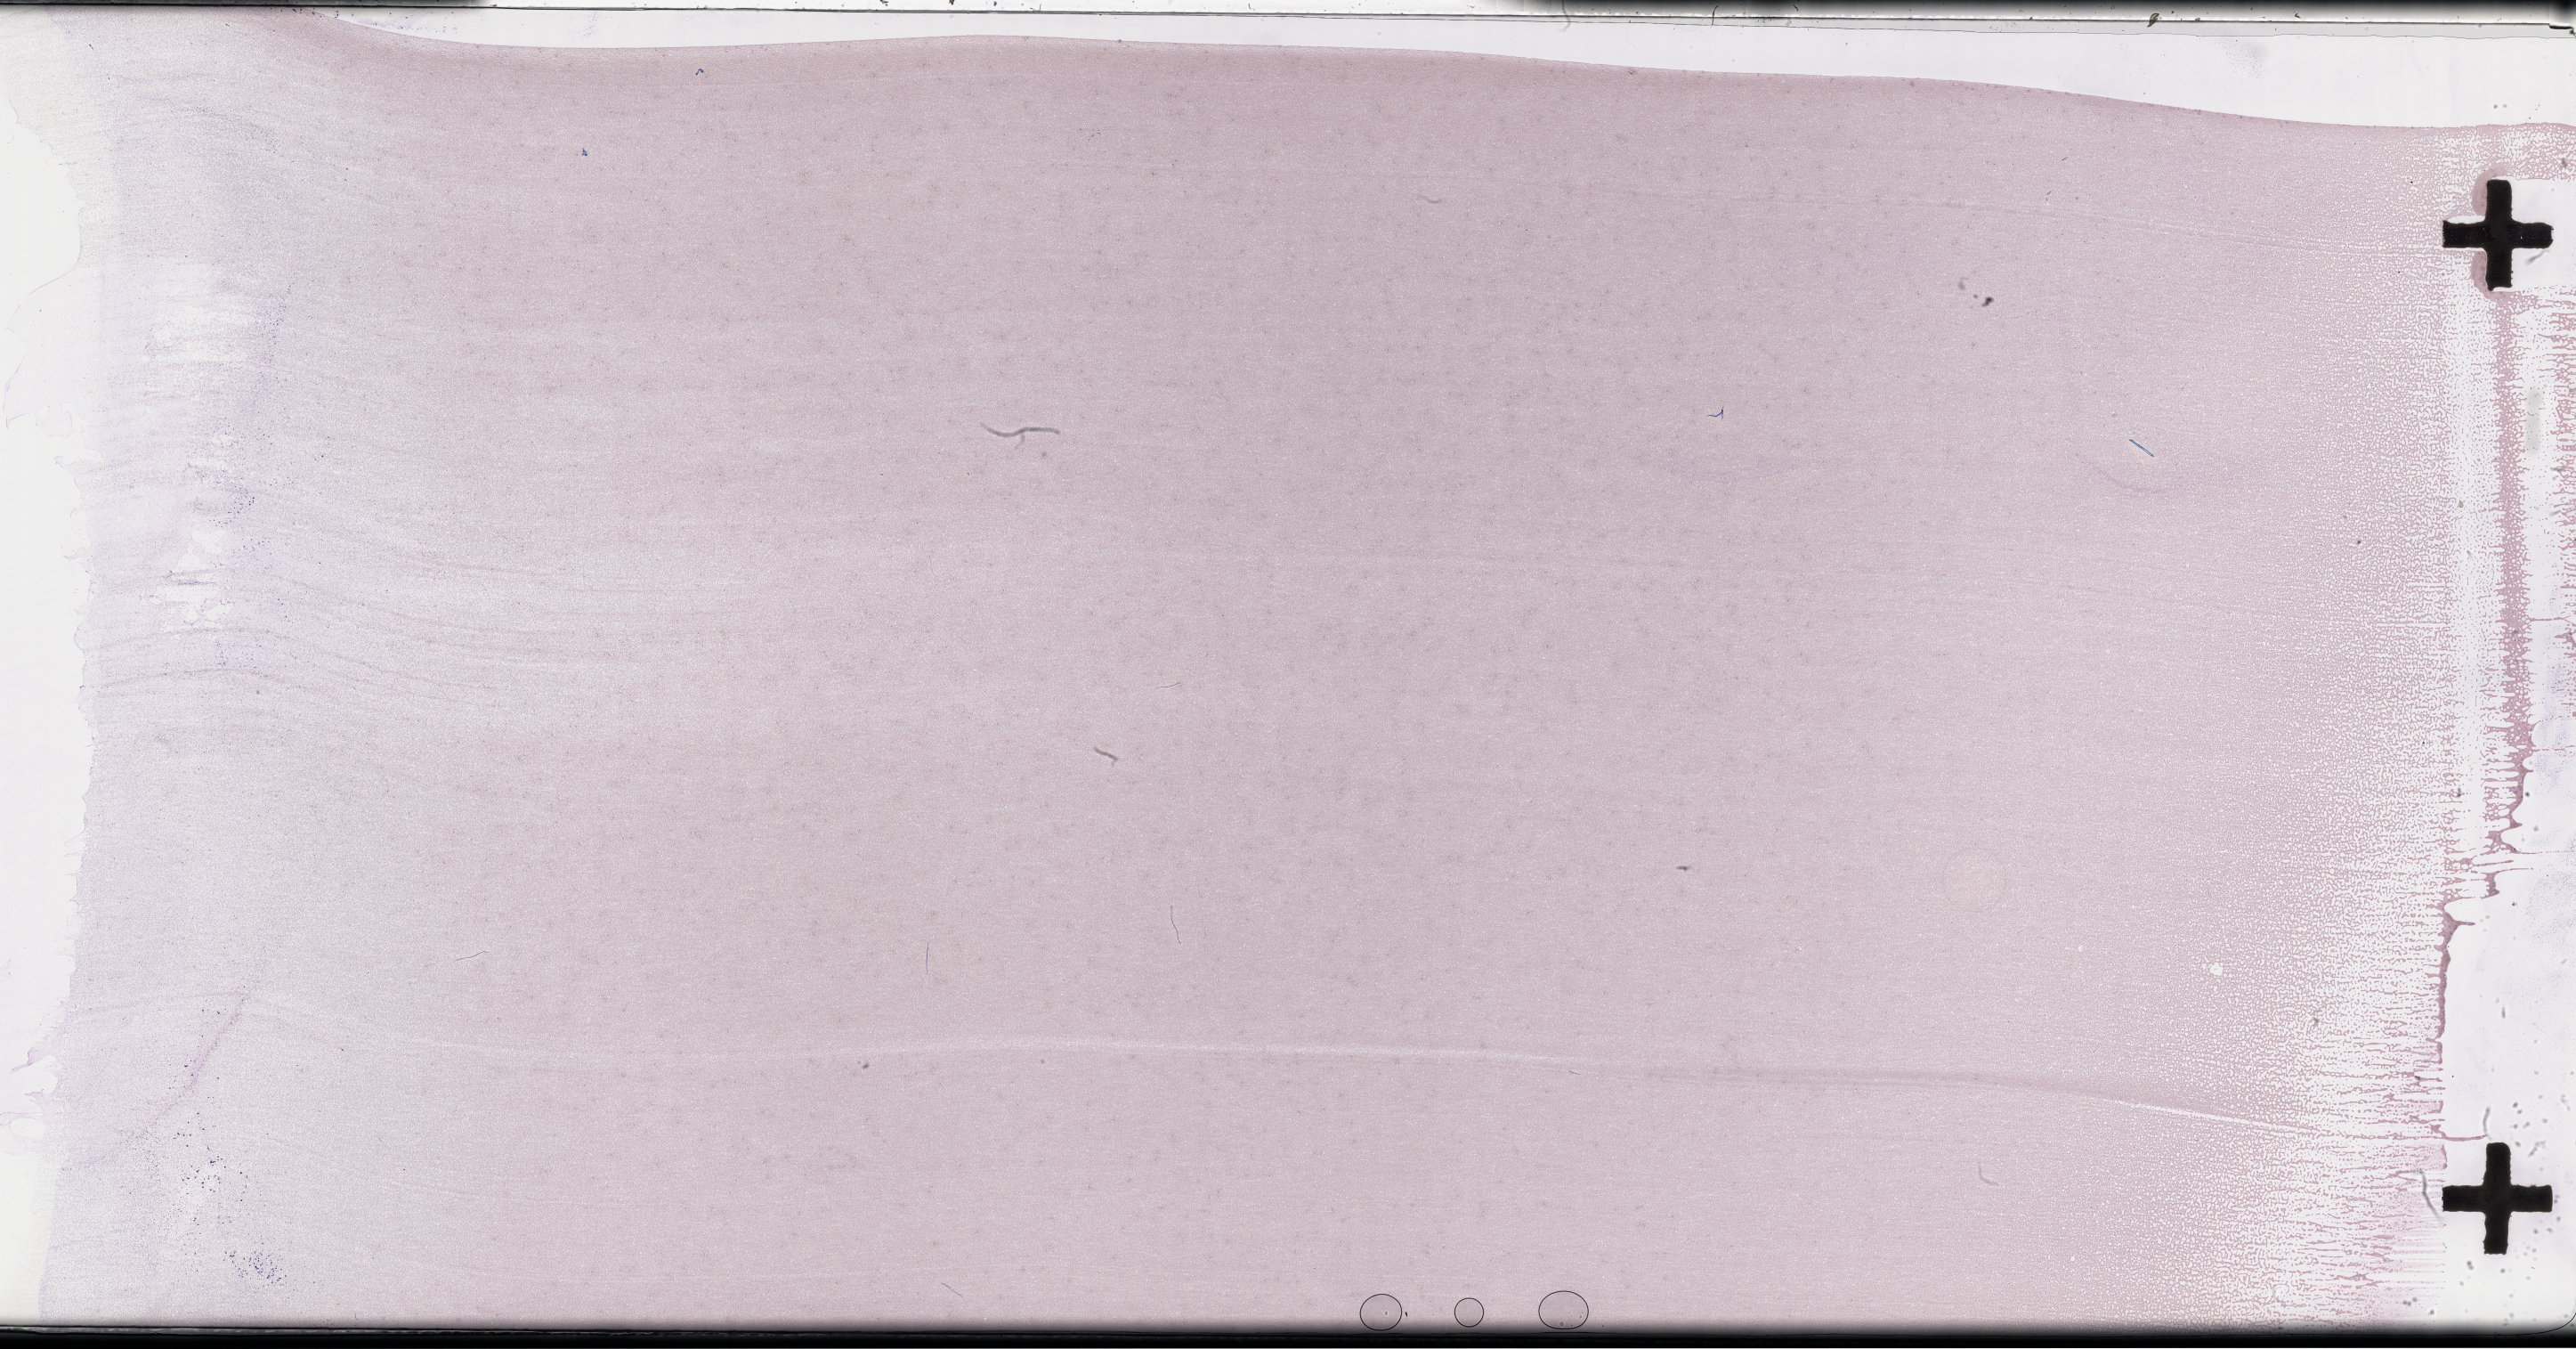
Whole-slide image of a whole blood smear, Wright-Giemsa stain — whole scanned area (about 46.7 x 24.5 mm) shown as a low-resolution overview; smear from an EDTA sample. Patient sex: male.
* from a patient with: Plasma Cell Myeloma